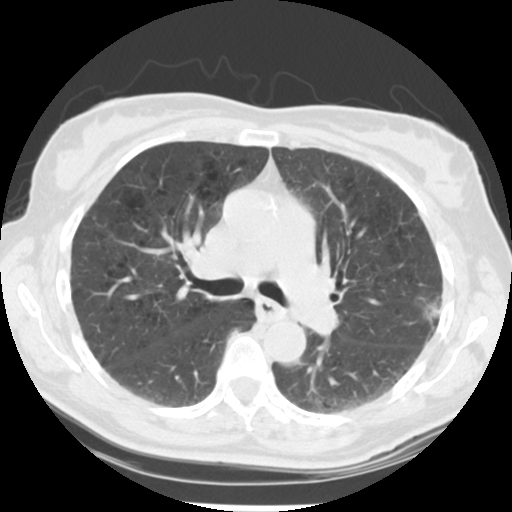
Chest CT (low-dose screening protocol), one axial image, second screening round (one year after baseline), lung window (W 1500 / L -600 HU), 2.5 mm slice thickness, slice 135 of 223 in the series. Female, age 61 years at enrolment. Current smoker at enrolment.
Expert reader's lesion annotation, bounding box [x1, y1, x2, y2] px = [406, 281, 464, 342]. Reader record for this screening exam (exam-level; its link to the box is not recorded): non-calcified nodule or mass ≥4 mm, left upper lobe, 15 × 15 mm, poorly defined margins, mixed attenuation, pre-existing on the prior screen: no.